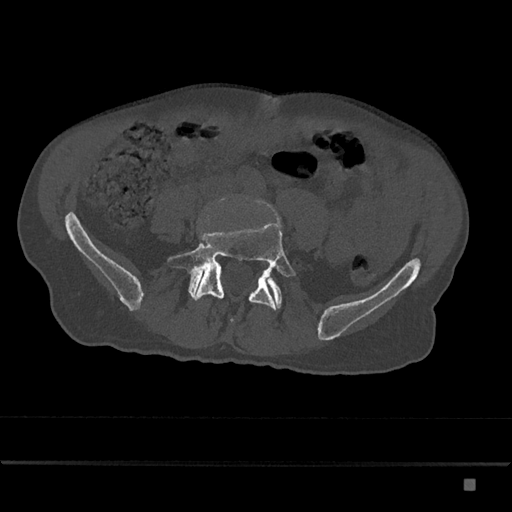
CT including the spine, one axial slice. Slice 280 of 797 in the series (ordered by position). 120 kVp. Bone window (W 1800 / L 400 HU). 0.5 mm slice thickness. 512 × 512 image matrix. Male patient, age 72 years. Case-level facts recorded for this patient, not image findings: primary cancer: prostate.
Outlined on this slice (semi-automatic segmentation, software-assisted and operator-edited):
- L5 vertebra: bounding box <167,221,296,323> (left, top, right, bottom; pixels)